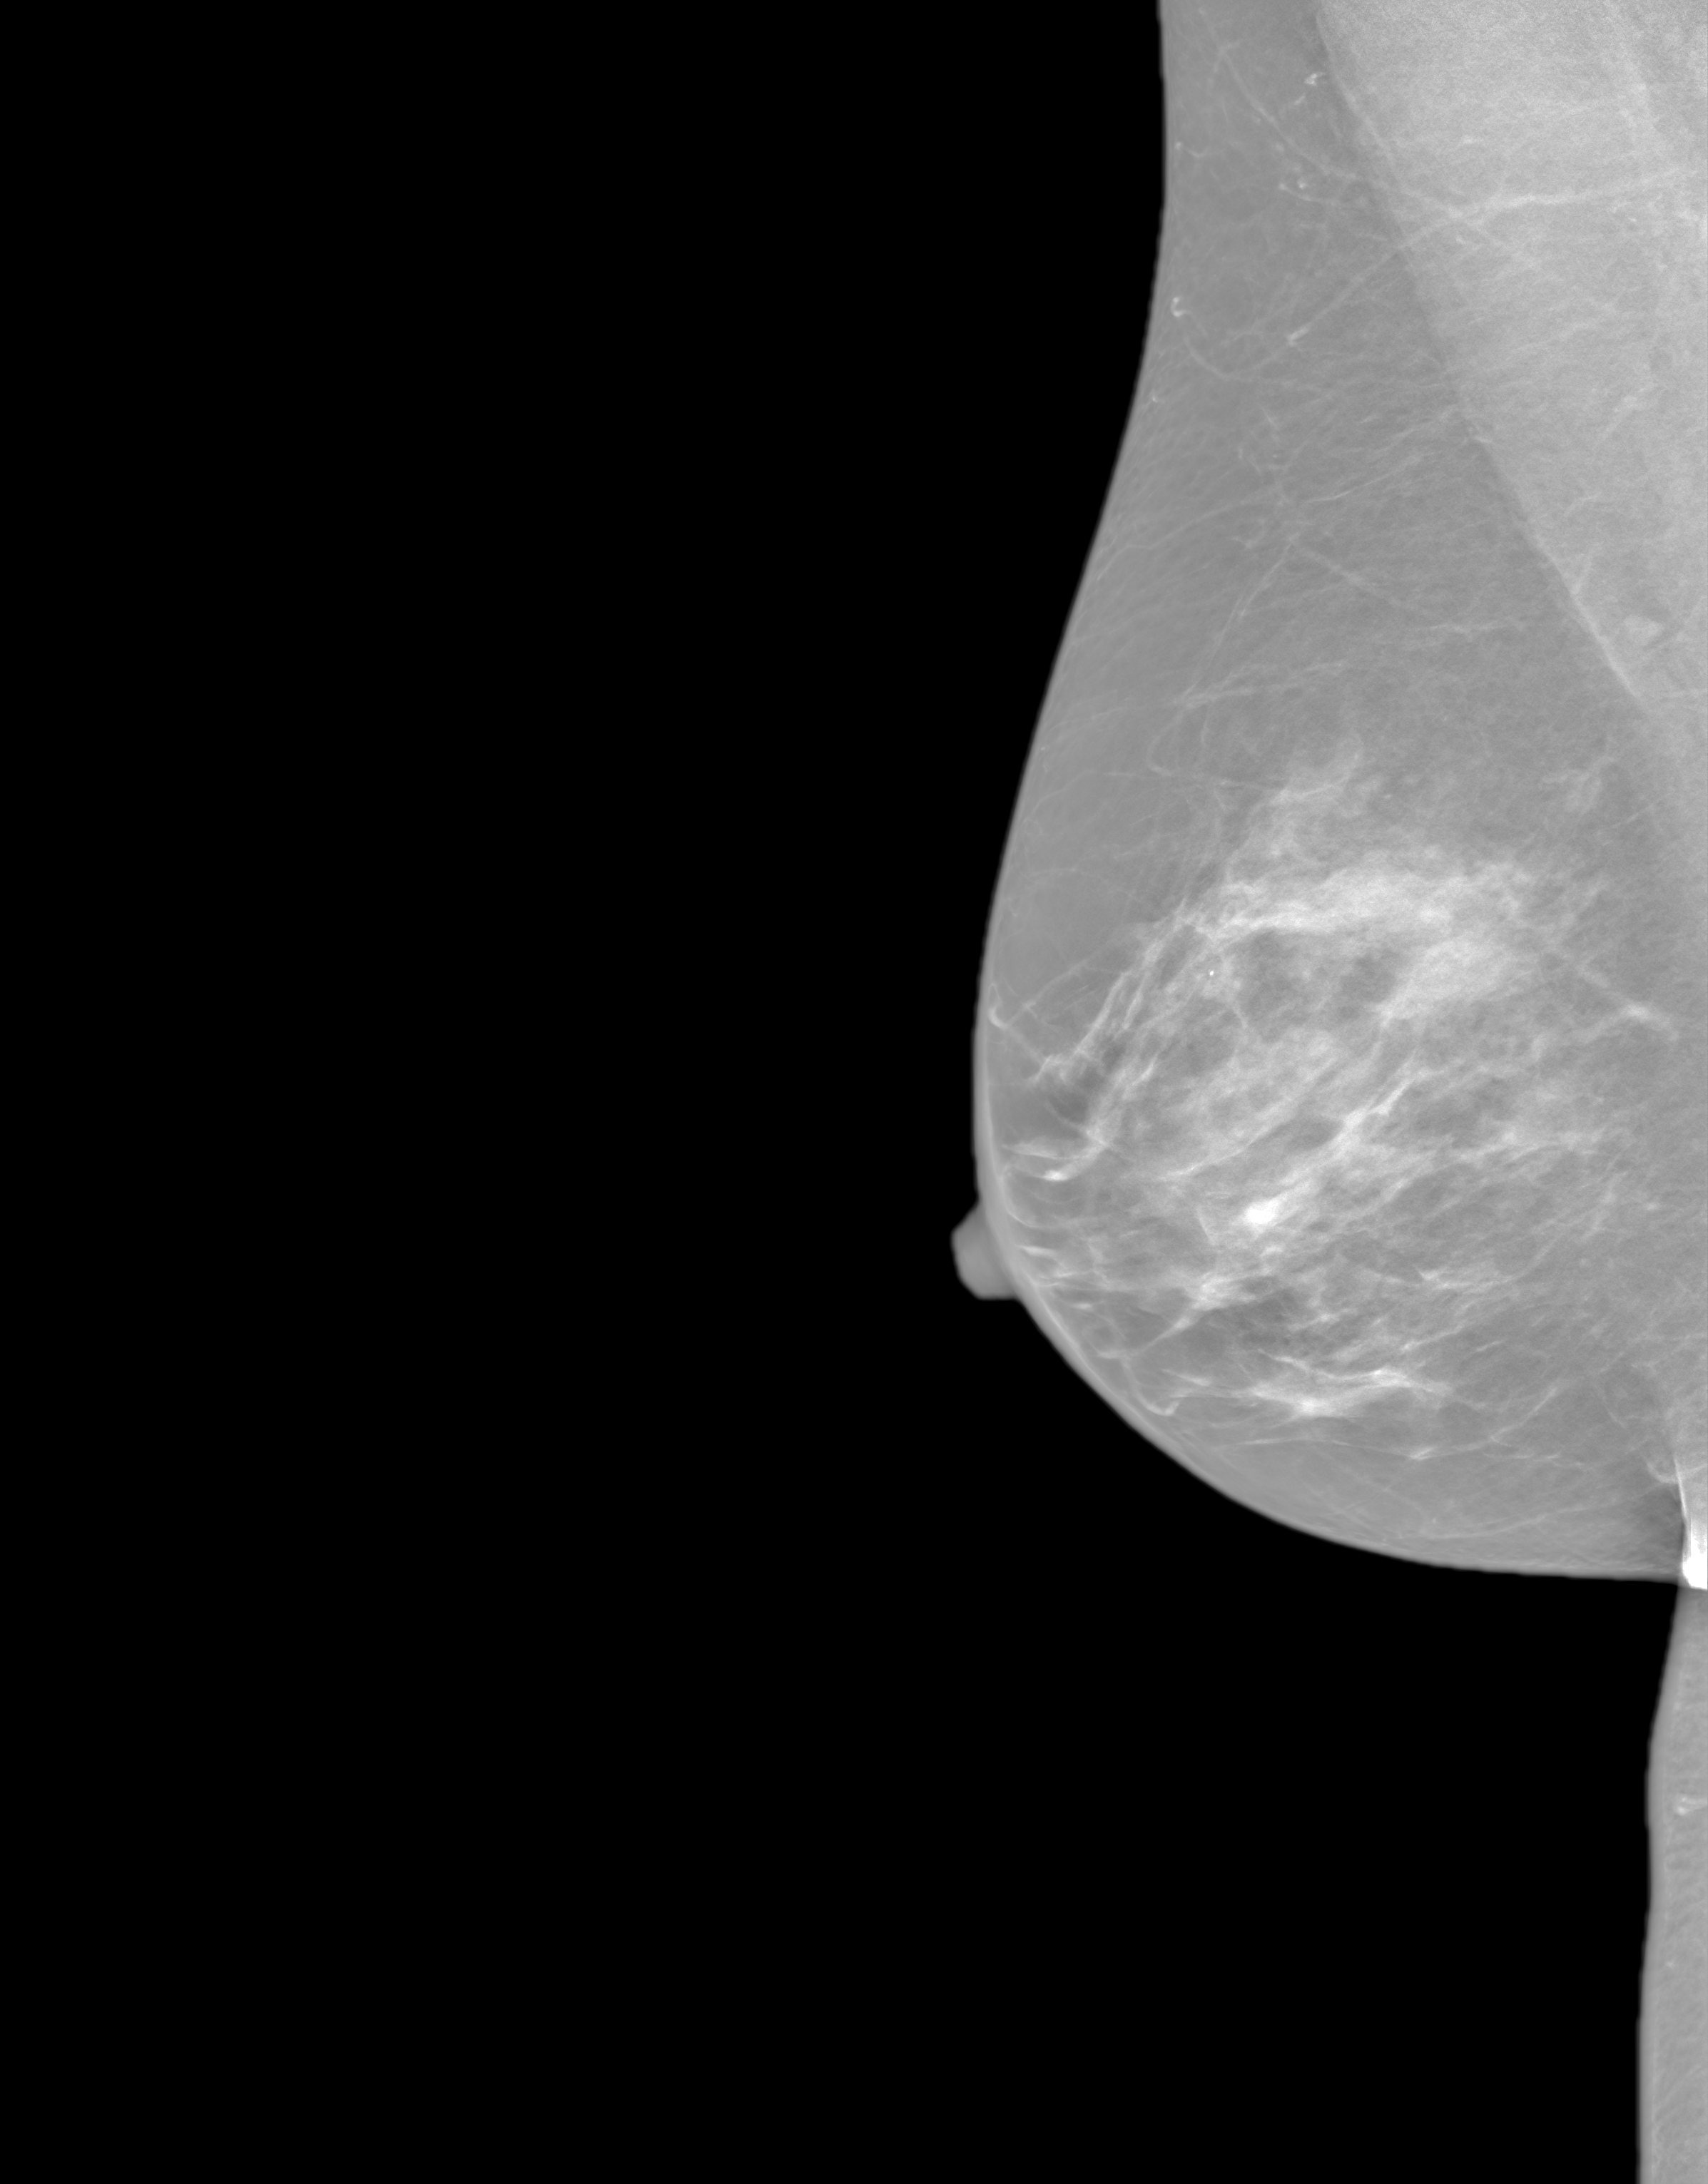
Annual screening mammography examination; system: SenoIris_1SP2(440). Patient aged 46 years (female).
Image type: synthesized 2-D view from tomosynthesis. Breast: right. Projection: mediolateral oblique (MLO) view.